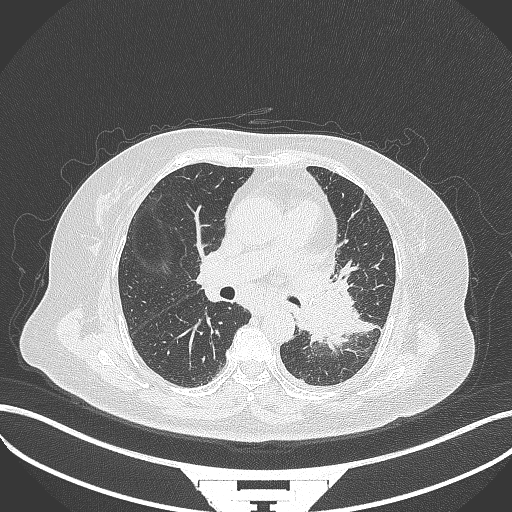
Chest CT, one axial slice; position 193 of 322 along the scan axis; 120 kVp; lung window (W 1500 / L -600 HU); 1 mm slice thickness; 512 × 512 image matrix. Patient: female, 69 years. From the clinical record (not read from this slice): clinical TNM (as recorded): T2b N3 M1.
Outlined on this slice (bounding box drawn by a radiologist):
- lung tumour (recorded histology: adenocarcinoma): box from (x=291, y=279) to (x=360, y=347) px